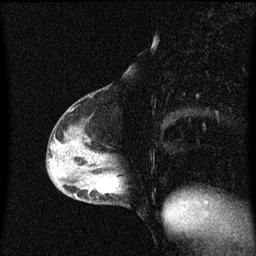
Breast MRI (dynamic contrast-enhanced), one sagittal slice. Slice 28 of 60 in the series (ordered by position). Dynamic contrast-enhanced series, image 2 of 3 at this slice position (ordered by acquisition). 1.5 T. TE 4.2 ms, TR 8.4 ms. 2 mm slice thickness. 256 × 256 image matrix, field of view 200 × 200 mm. Female patient, age 40 years.
Outlined on this slice (semi-automatic segmentation, software-assisted and operator-edited):
- analysis volume of interest (the breast-tissue region the enhancement analysis was run in; not a lesion): bounding box [x1, y1, x2, y2] px = [82, 172, 125, 205]
- tumour enhancement mask (voxels above the 70 % enhancement threshold inside the analysis volume of interest): [114, 176, 119, 187]